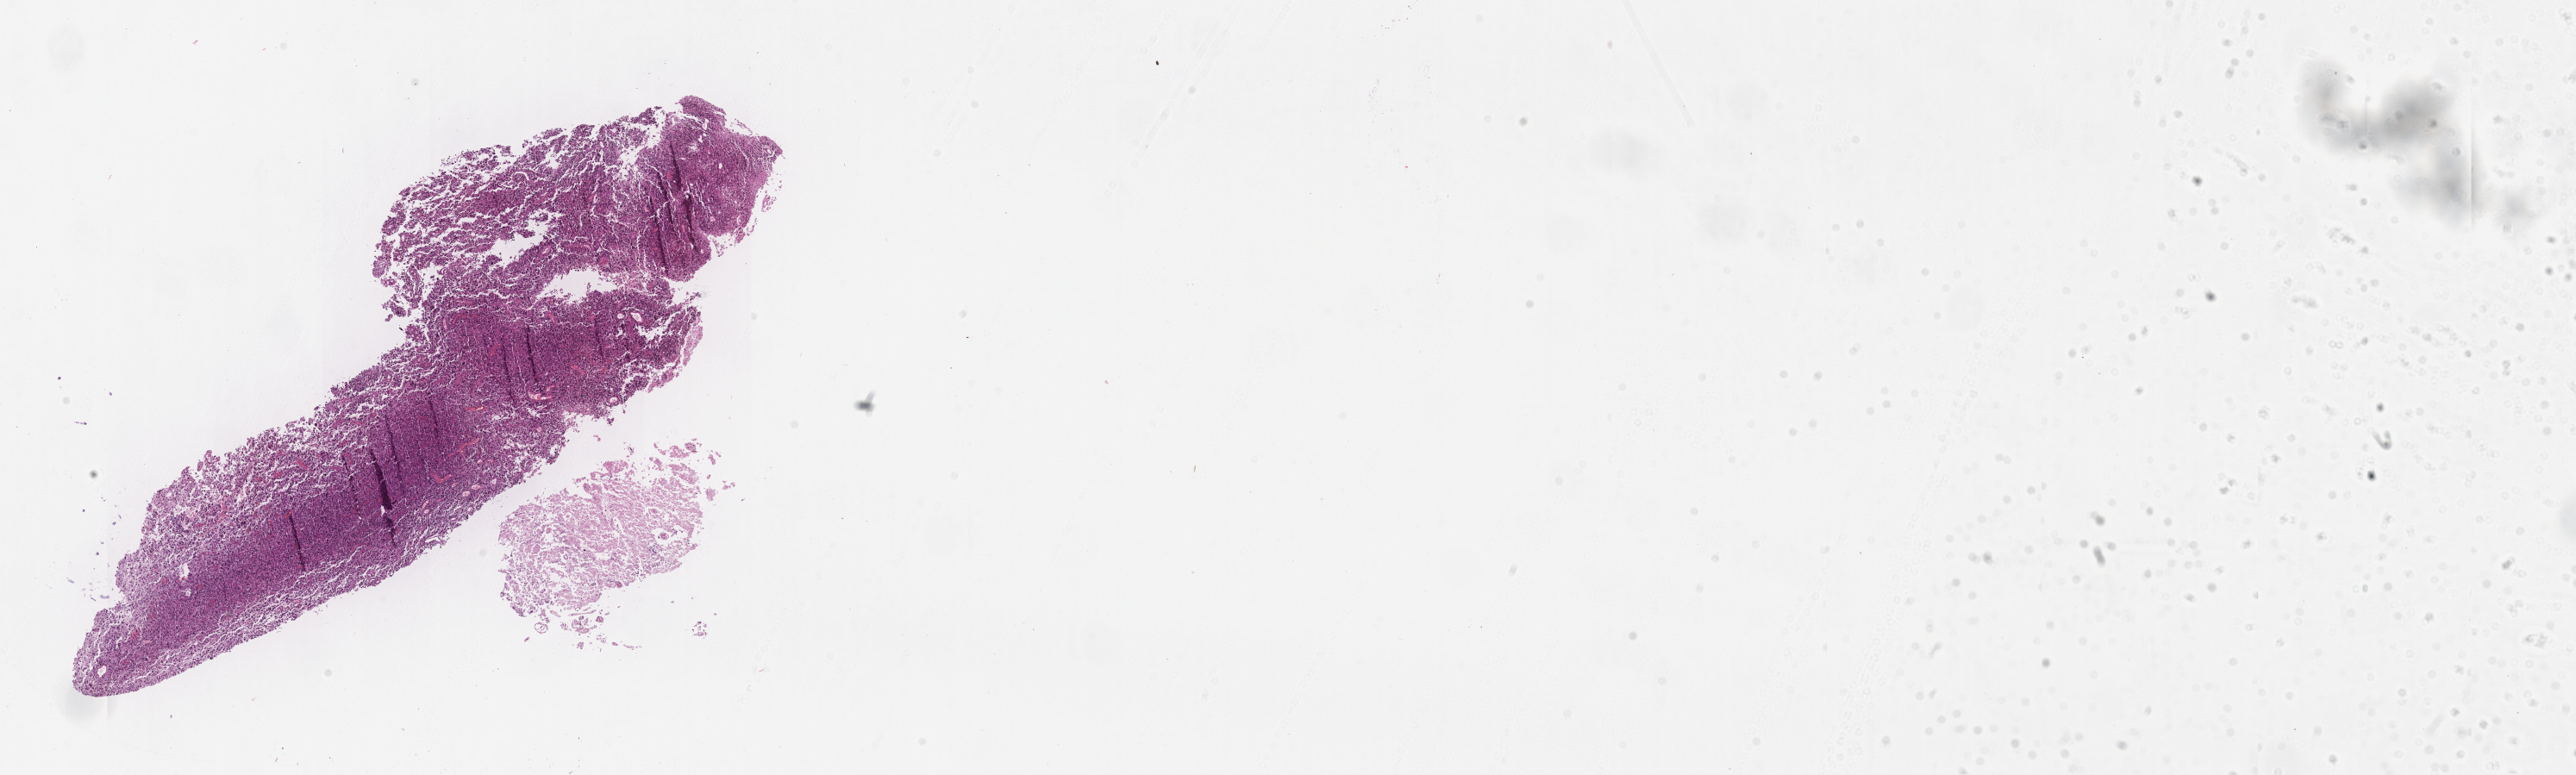
Whole-slide histology image, H&E, shown as a low-resolution overview of the whole scanned area (about 24.1 x 7.2 mm), tumour tissue sample, sampled site: brain. Patient: male, age 65 years. Pathologist review of this section (percent, as recorded): tumour nuclei 75%, necrosis 10%.
Histologic diagnosis: Glioblastoma. Primary tumour site (as recorded): temporal lobe.